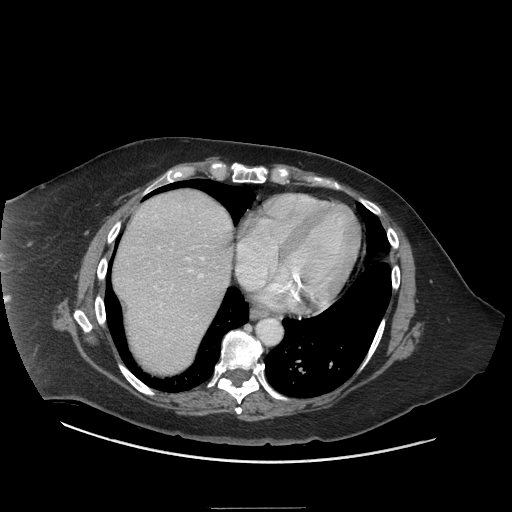
Contrast-enhanced abdominal CT (liver protocol), one axial slice. Position 65 of 81 along the scan axis. 140 kVp. Soft-tissue window (W 400 / L 40 HU). 2.5 mm slice thickness. 512 × 512 image matrix, field of view 440 × 440 mm. Case-level facts recorded for this patient, not image findings: diagnosis: hepatocellular carcinoma (patient treated with transarterial chemoembolisation; whether this scan precedes or follows treatment is not stated here); TNM stage (as recorded): Stage-II; Child-Pugh class: A; tumour differentiation: moderately differentiated; tumour nodularity: multinodular.
Annotated regions visible in this slice (semi-automatic segmentation, software-assisted and operator-edited):
- abdominal aorta: bounding box <257,318,281,345> (left, top, right, bottom; pixels)
- liver parenchyma outside the tumour (the mass and vessels are separate outlines, so this box may not span the whole liver): <112,190,231,374>
- liver vessels: <141,206,229,334>